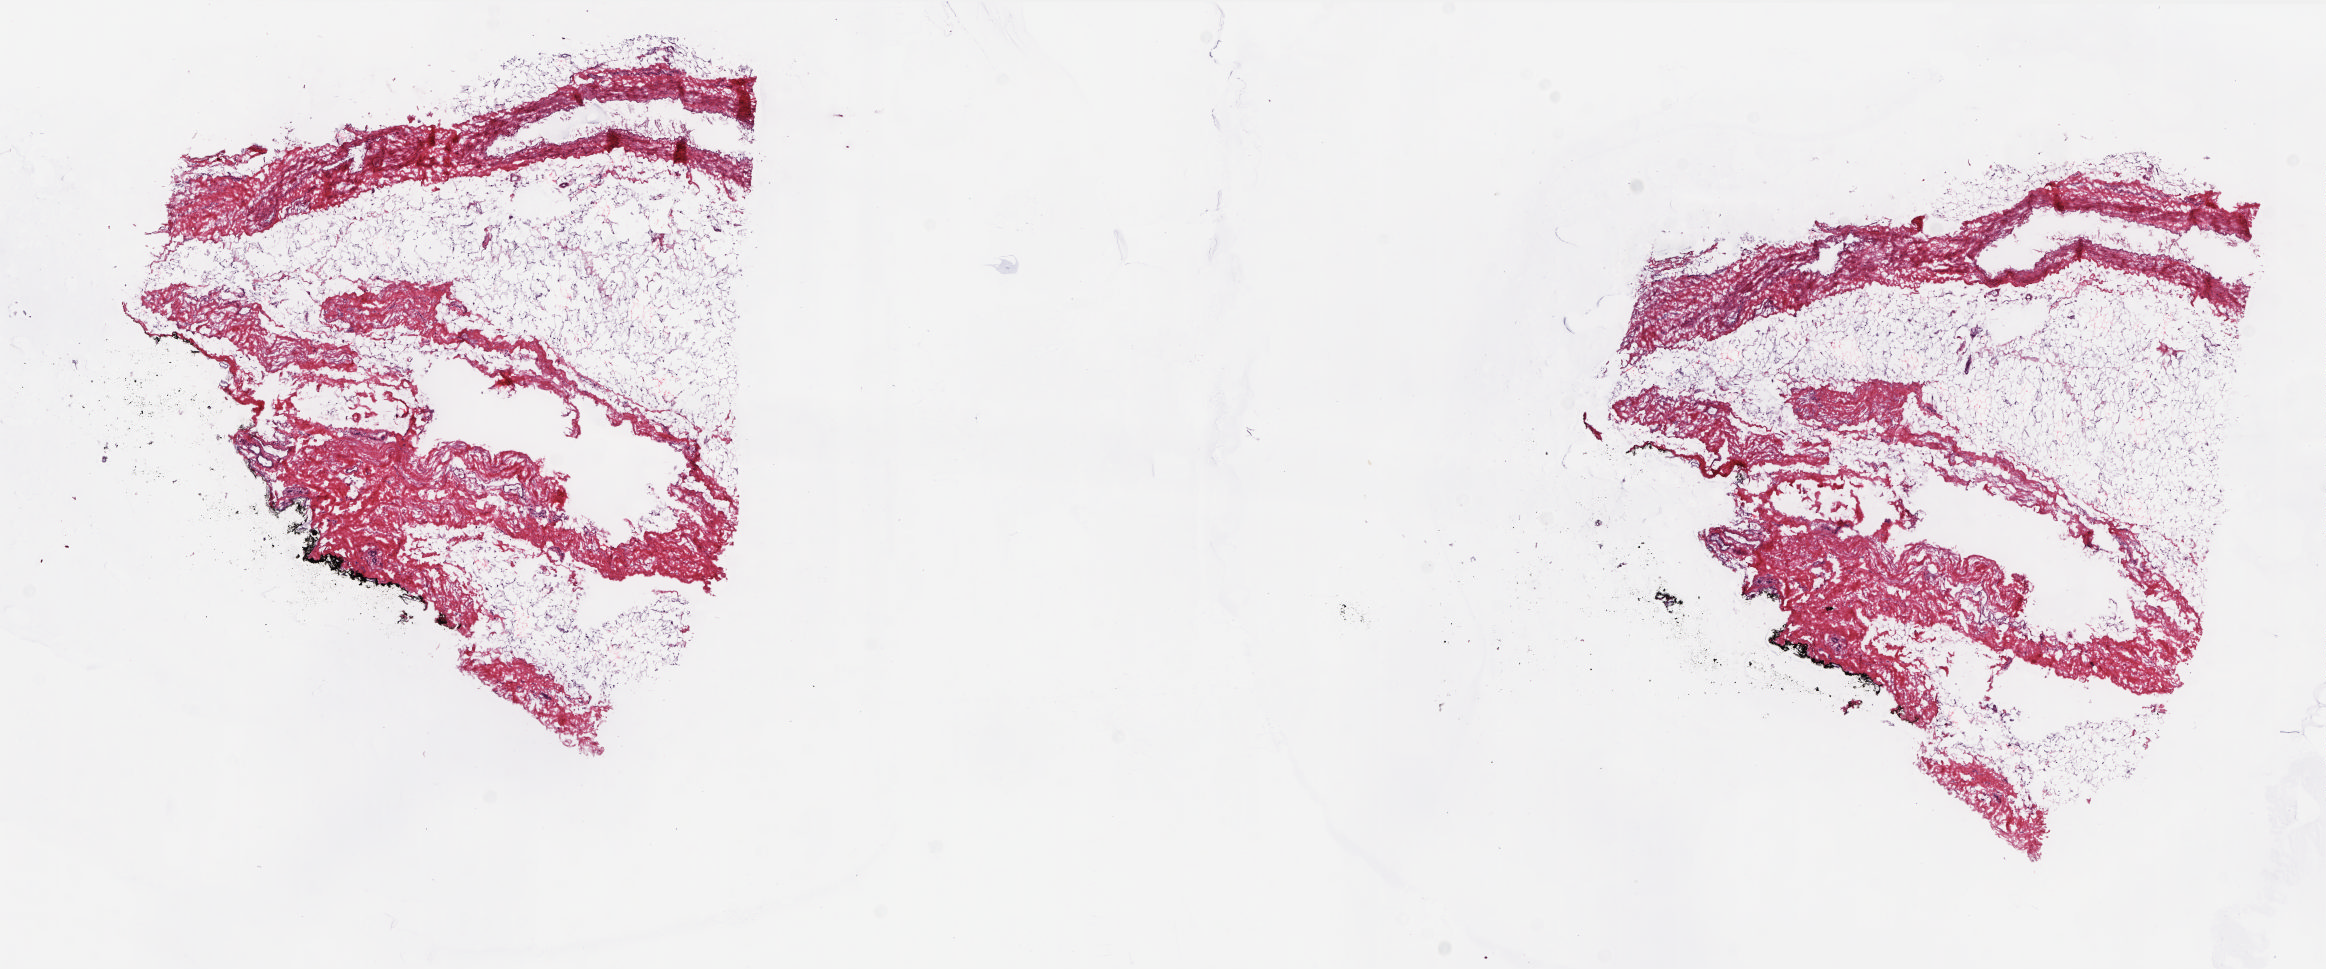
H&E whole-slide image, whole scanned area (about 18.8 x 7.8 mm) shown as a low-resolution overview, frozen section, breast, solid tissue normal (non-tumour tissue) sample. Female, age 74 years at initial diagnosis. Composition of this section per pathologist review: tumour cells 0%, tumour nuclei 0%, normal cells 100%, stromal cells 0%, necrosis 0%. Infiltration values recorded for this section: lymphocyte infiltration 0%, monocyte infiltration 0%, neutrophil infiltration 0%.
This section: solid tissue normal (non-tumour) sample from the same patient. Patient diagnosis: Lobular carcinoma, NOS.